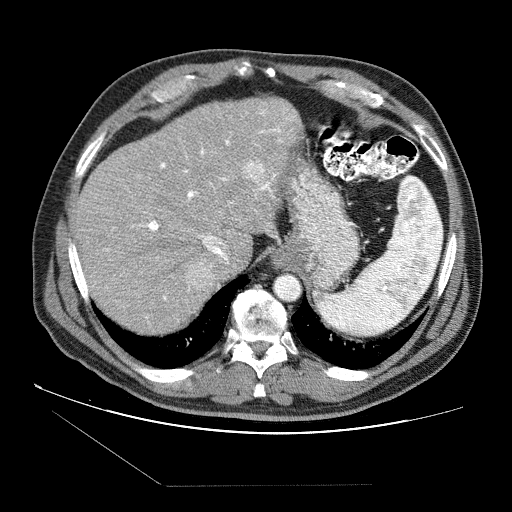
Contrast-enhanced abdominal CT (liver protocol), one axial slice. Position 62 of 87 along the scan axis. Reconstruction kernel STANDARD. Soft-tissue window (W 400 / L 40 HU). 2.5 mm slice thickness. 512 × 512 image matrix, field of view 400 × 400 mm. Case-level facts recorded for this patient, not image findings: diagnosis: hepatocellular carcinoma (patient treated with transarterial chemoembolisation; whether this scan precedes or follows treatment is not stated here); TNM stage (as recorded): Stage-II; Child-Pugh class: B; tumour differentiation: no biopsy; tumour nodularity: multinodular.
Annotated regions visible in this slice (semi-automatically segmented with operator editing):
- liver parenchyma outside the tumour (the mass and vessels are separate outlines, so this box may not span the whole liver): bounding box [x1, y1, x2, y2] px = [74, 96, 302, 334]
- mass: [184, 161, 263, 290]
- liver vessels: [103, 110, 294, 300]